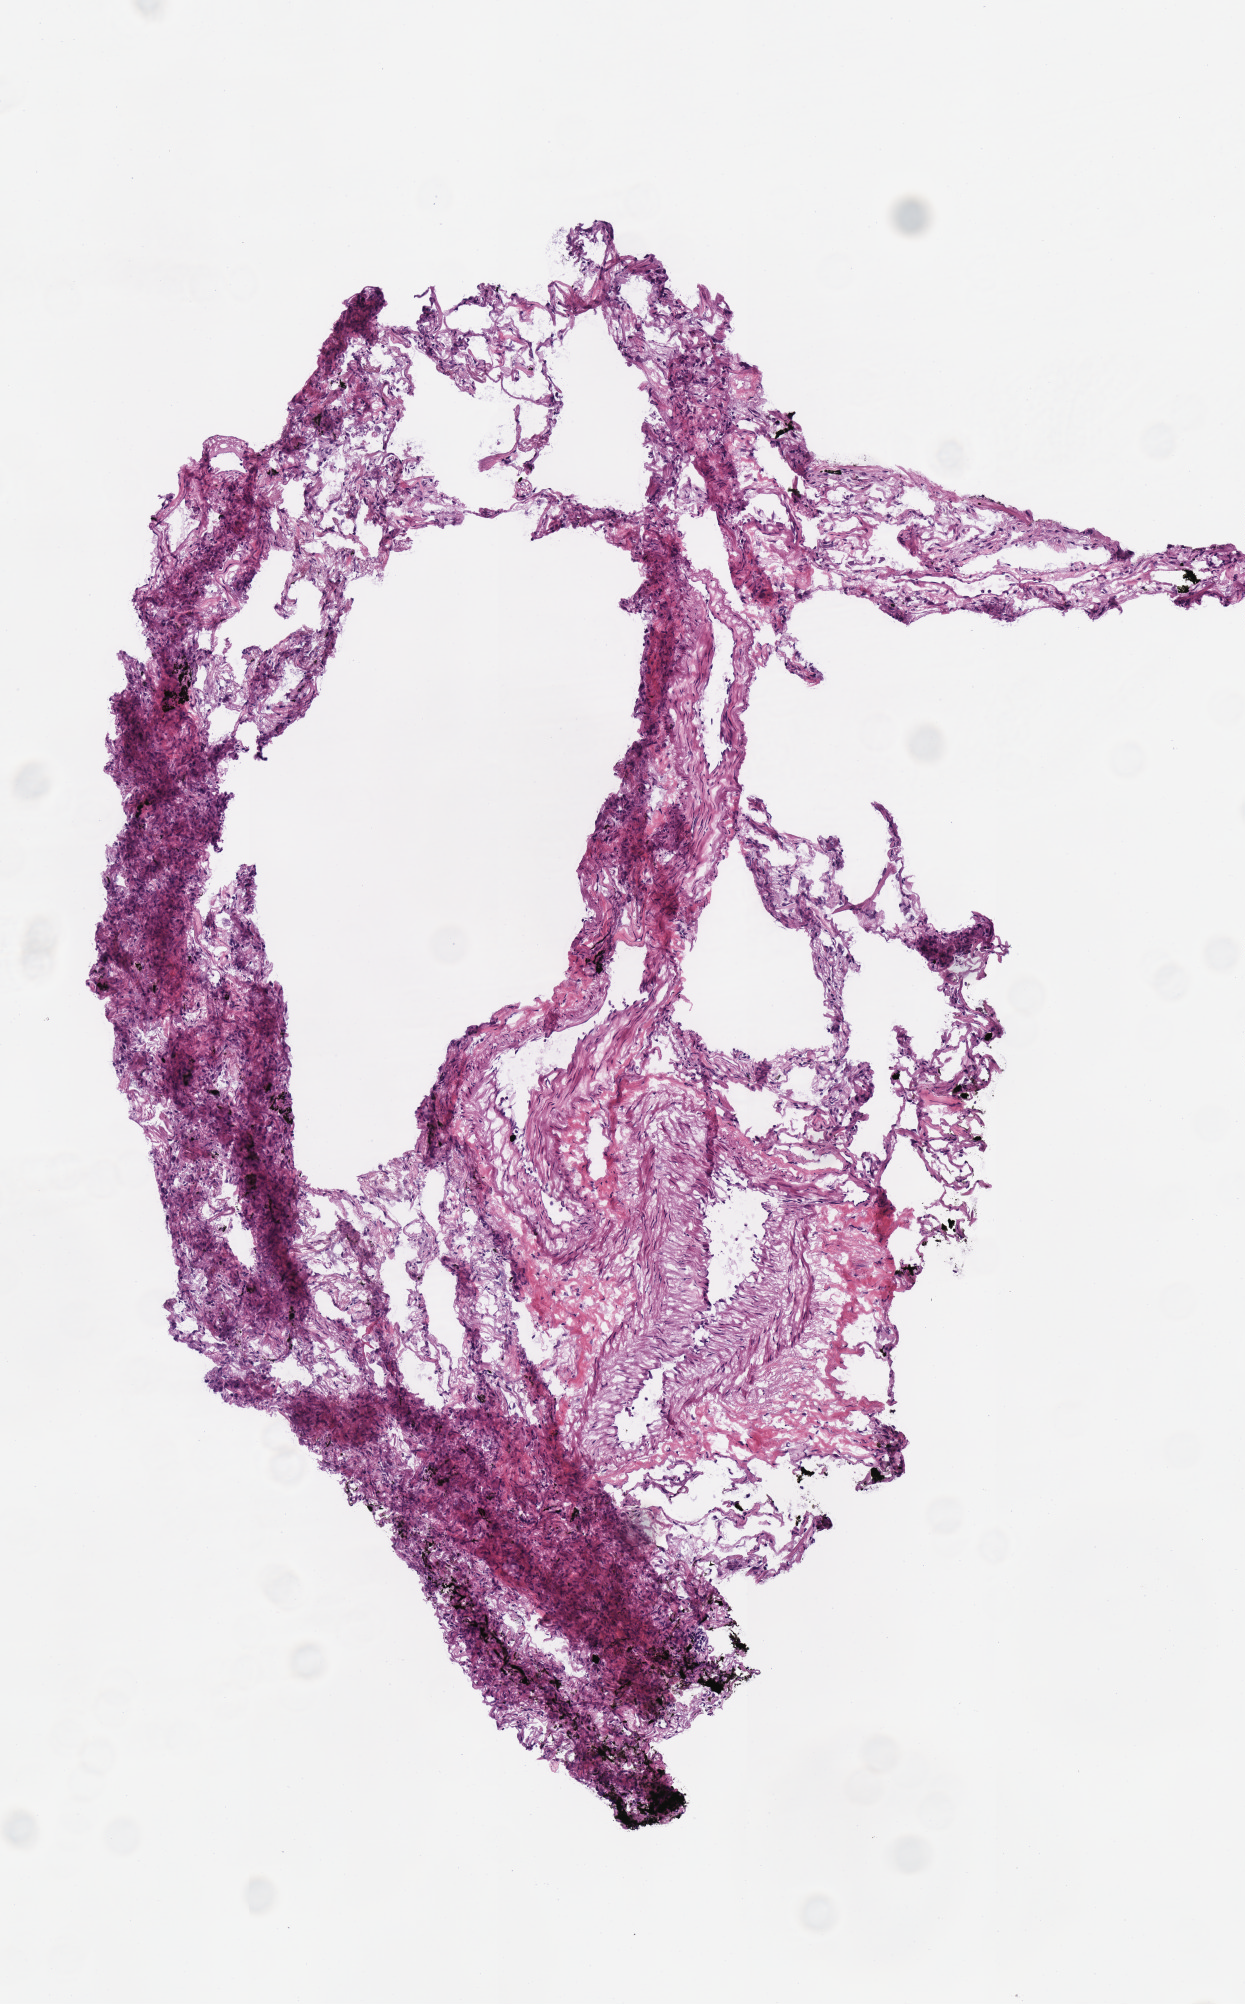
Whole-slide histology image, H&E — low-resolution overview of the scanned area, about 2.4 x 3.9 mm (acquisition: 40x scan); frozen section; sample: solid tissue normal (non-tumour tissue), lung. Female, age 76 years at initial diagnosis.
This section: solid tissue normal sample (biorepository sample class). Patient diagnosis: Adenocarcinoma, NOS (upper lobe, lung).